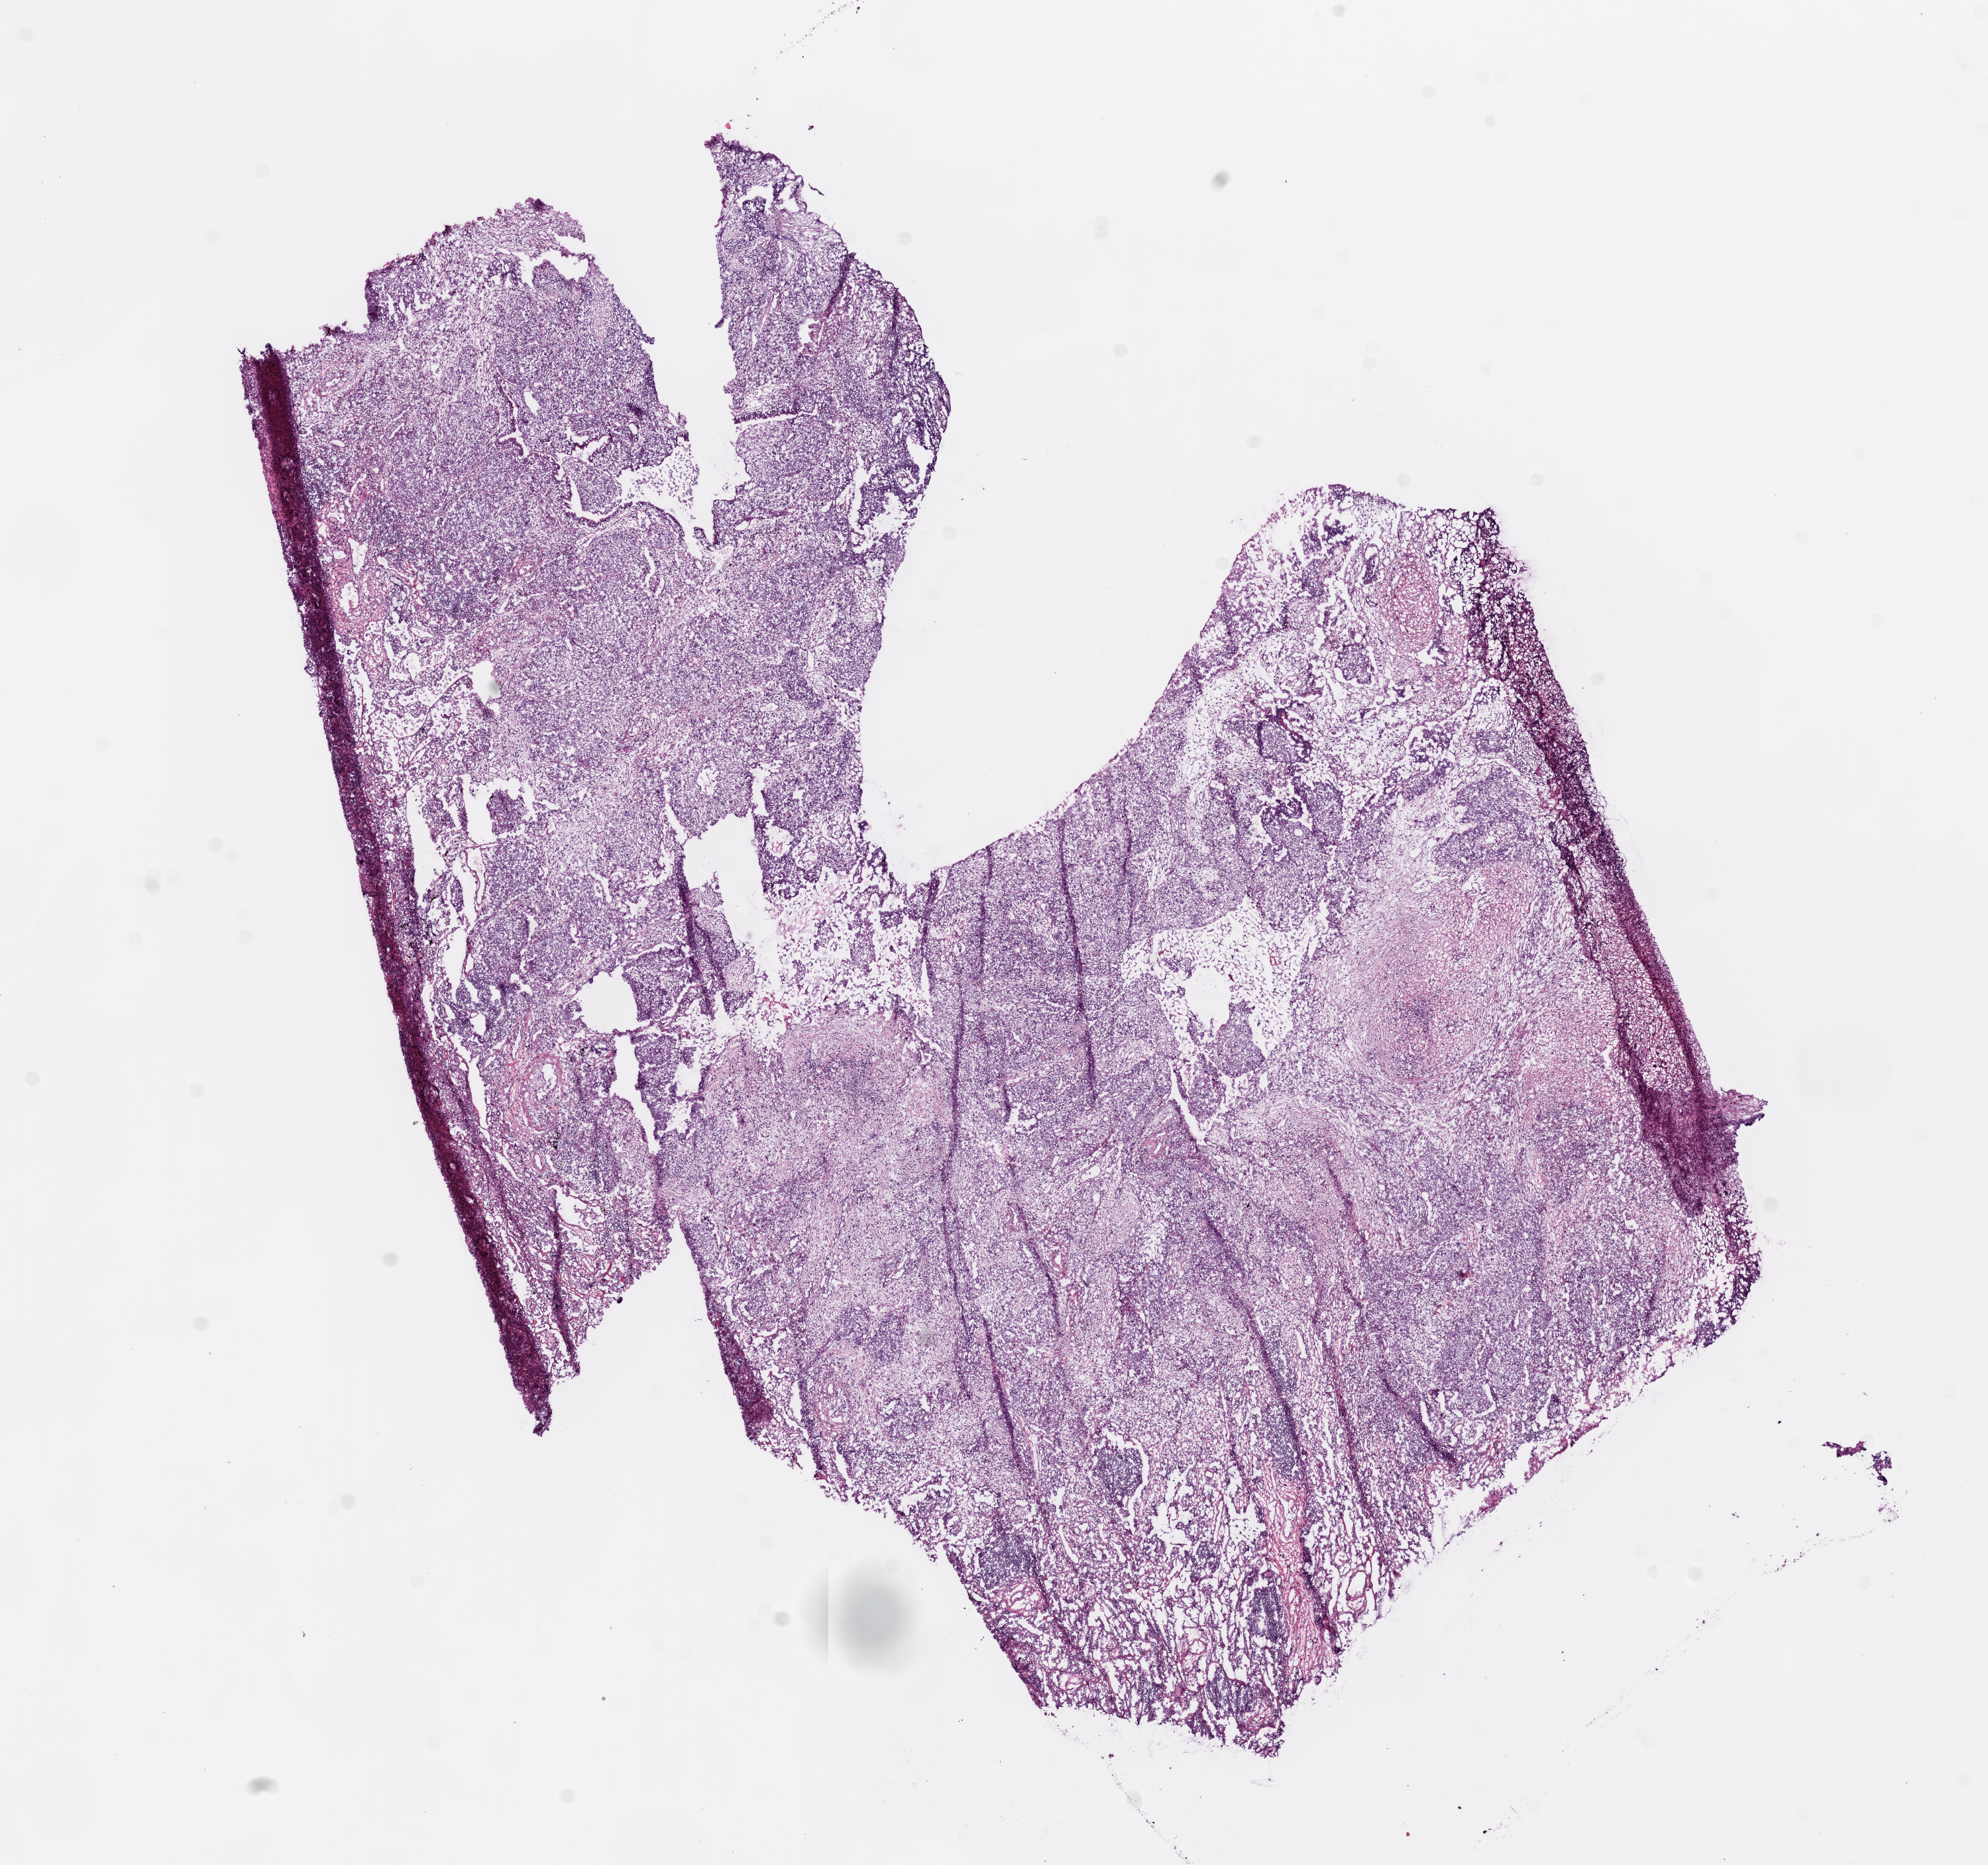
Whole-slide histology image, H&E-stained, whole scanned area (about 12.0 x 11.3 mm) shown as a low-resolution overview, frozen section from the bottom of the tissue portion, sample: primary tumour, lung. Female patient; age at initial diagnosis 60 years. Composition of this section per pathologist review: tumour cells 72%, tumour nuclei 80%, normal cells 5%, stromal cells 15%, necrosis 8%.
- AJCC pathologic stage: IB
- diagnosis: Squamous cell carcinoma, NOS (lower lobe, lung)
- laterality: right